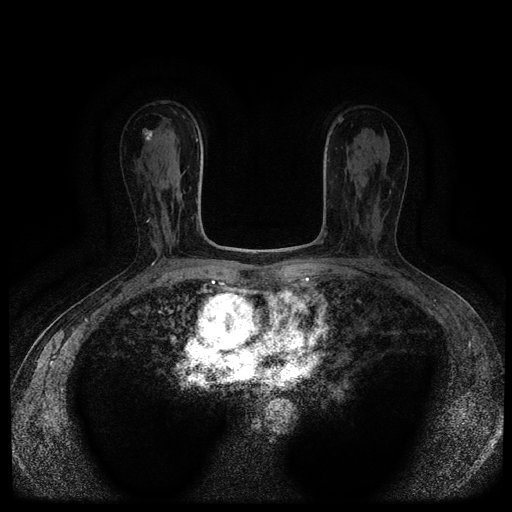
Breast MRI (dynamic contrast-enhanced, multi-phase), one axial slice. Position 59 of 116 along the scan axis. Dynamic contrast-enhanced series, time point 2 of 5 at this slice position (early post-contrast). 1.5 T. TE 2.7 ms, TR 5.4 ms. 512 × 512 image matrix, field of view 330 × 330 mm. Female patient, age 63 years.
Annotated regions visible in this slice (semi-automatically segmented with operator editing):
- breast lesion (labelled benign in the annotation): box from (x=142, y=128) to (x=153, y=141) px